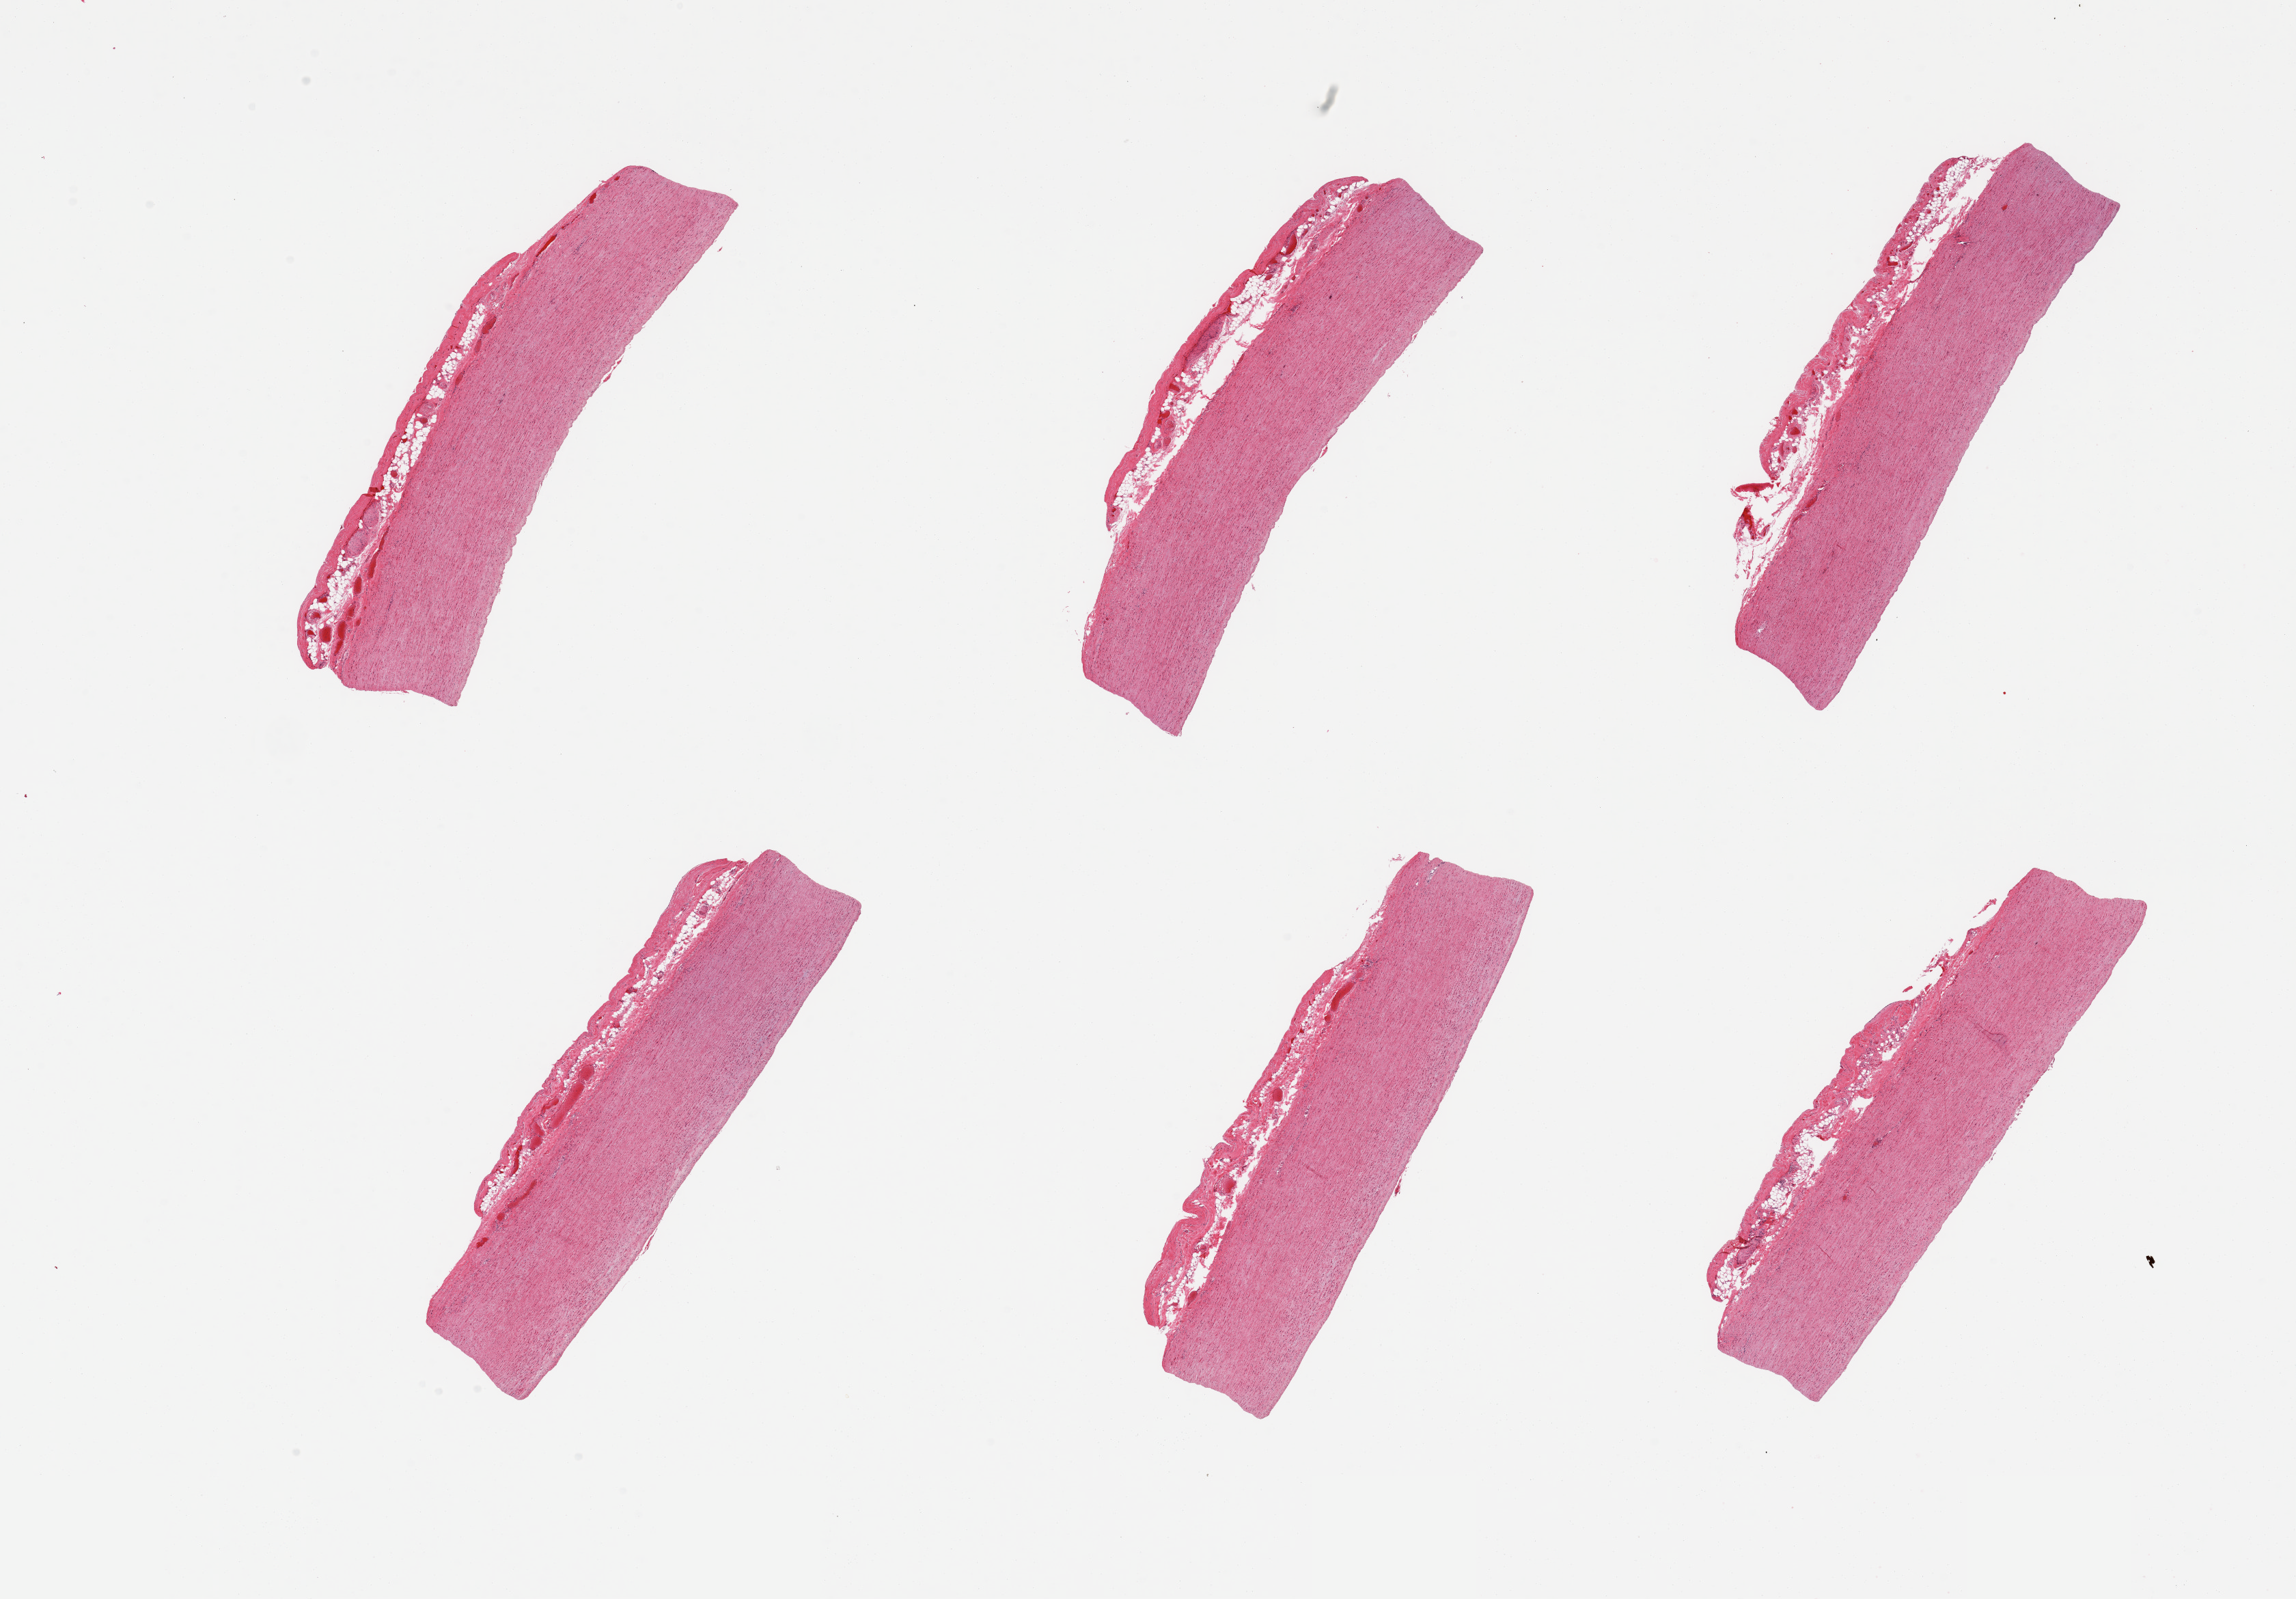
Digitized hematoxylin and eosin (H&E)-stained section — low-resolution overview of the scanned area, about 26.6 x 18.5 mm (from a 20x scan). PAXgene-fixed, paraffin-embedded tissue. Target tissue: aorta. Donor tissue sample. Male donor.
Pathologist's review note for this sample: 6 pieces; no plaques.